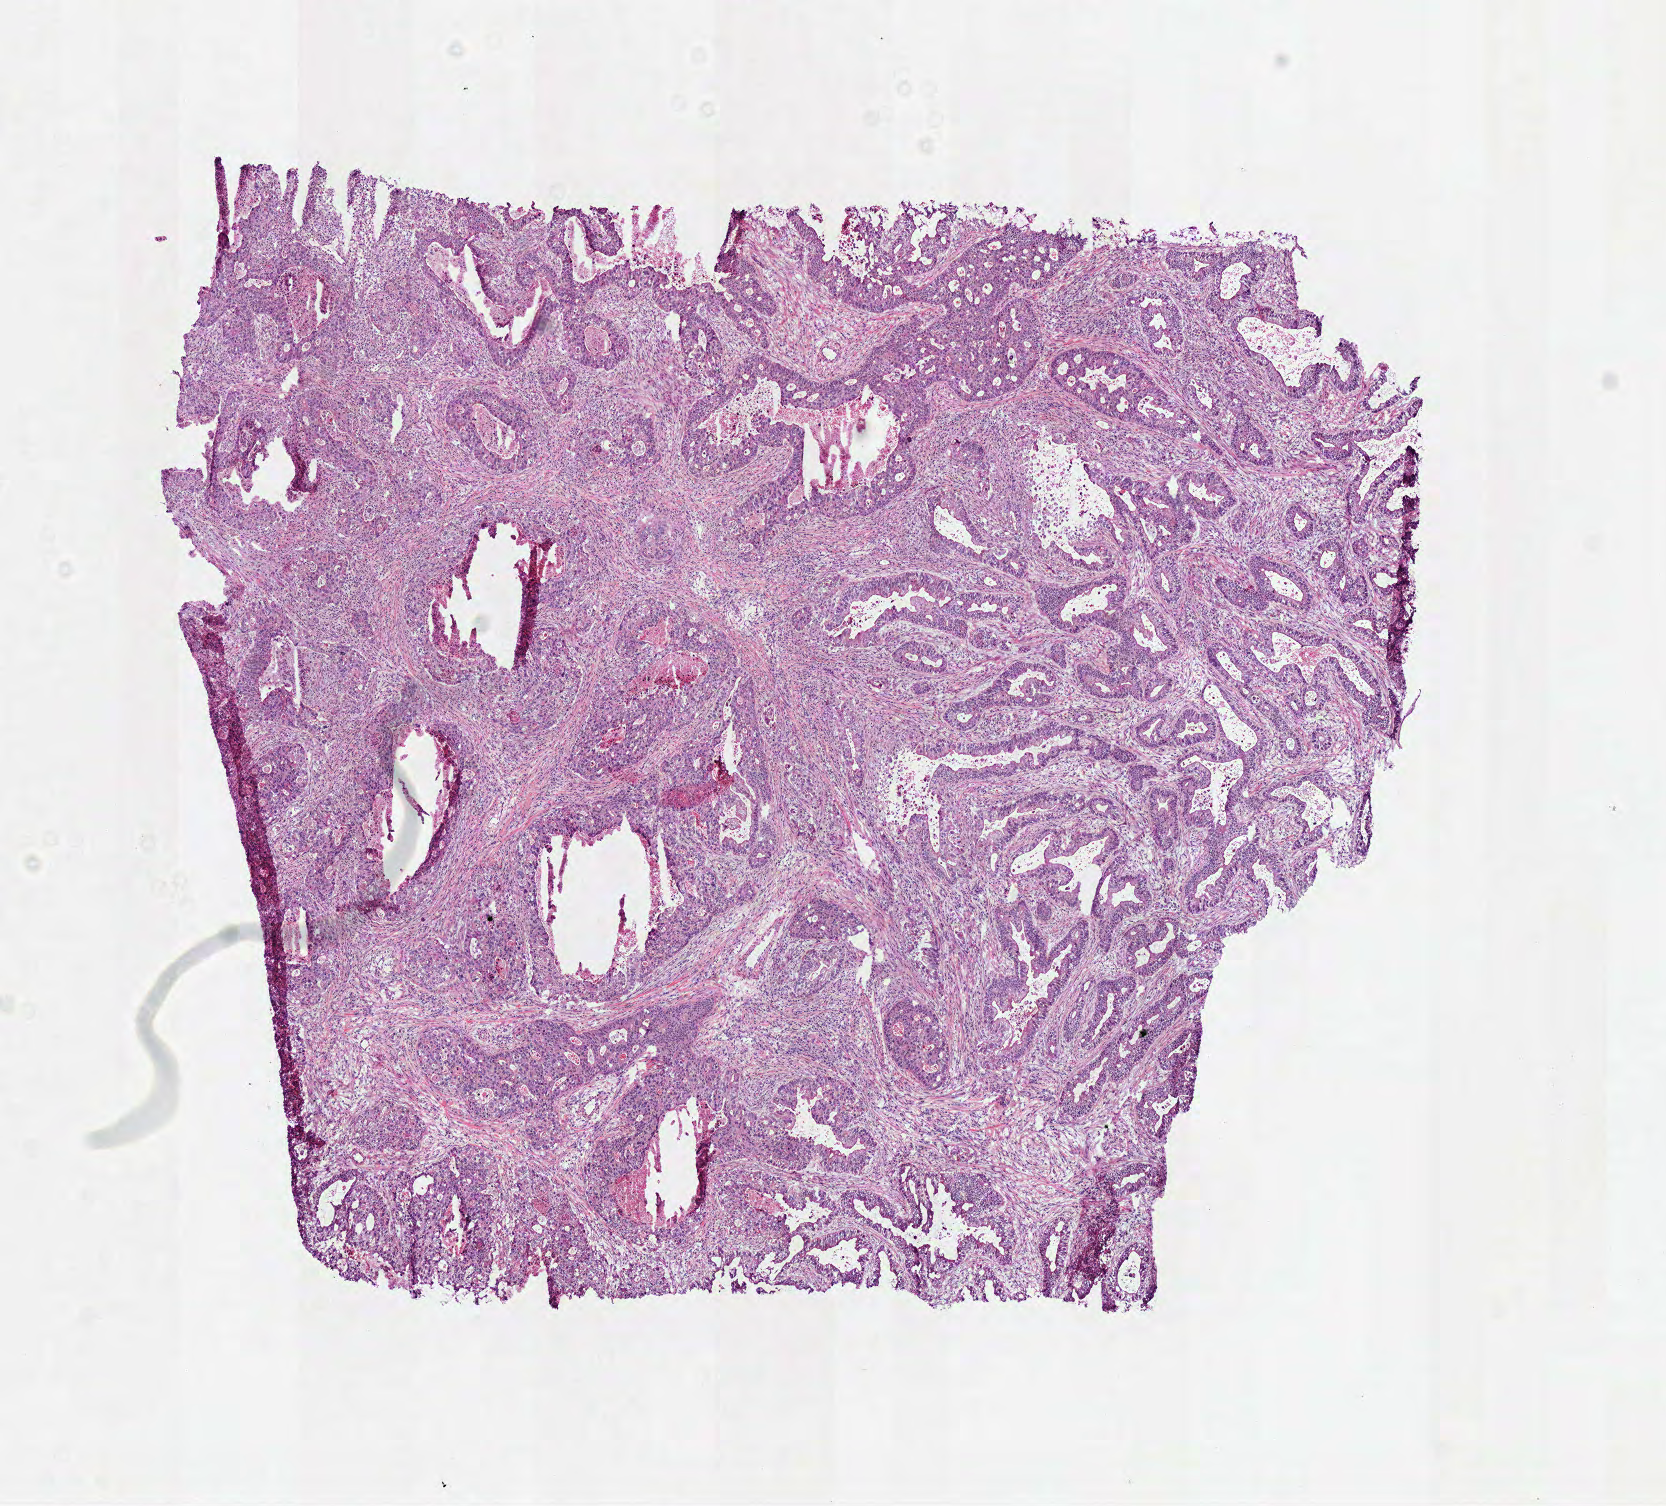
Whole-slide histology image, H&E, a low-resolution overview of the entire scanned area, about 6.6 x 5.9 mm (from a 40x scan). Frozen section. Primary tumour sample from the stomach. Patient: female, age at initial diagnosis 70 years. Histologic grade: G2 (moderately differentiated). Pathologist review of this section (percent, as recorded): tumour cells 70%, tumour nuclei 55%, normal cells 0%, stromal cells 20%, necrosis 10%.
AJCC pathologic stage: IIB (7th edition). Lymph nodes positive (case pathology): 5 of 19 examined. Histologic diagnosis: Tubular adenocarcinoma.